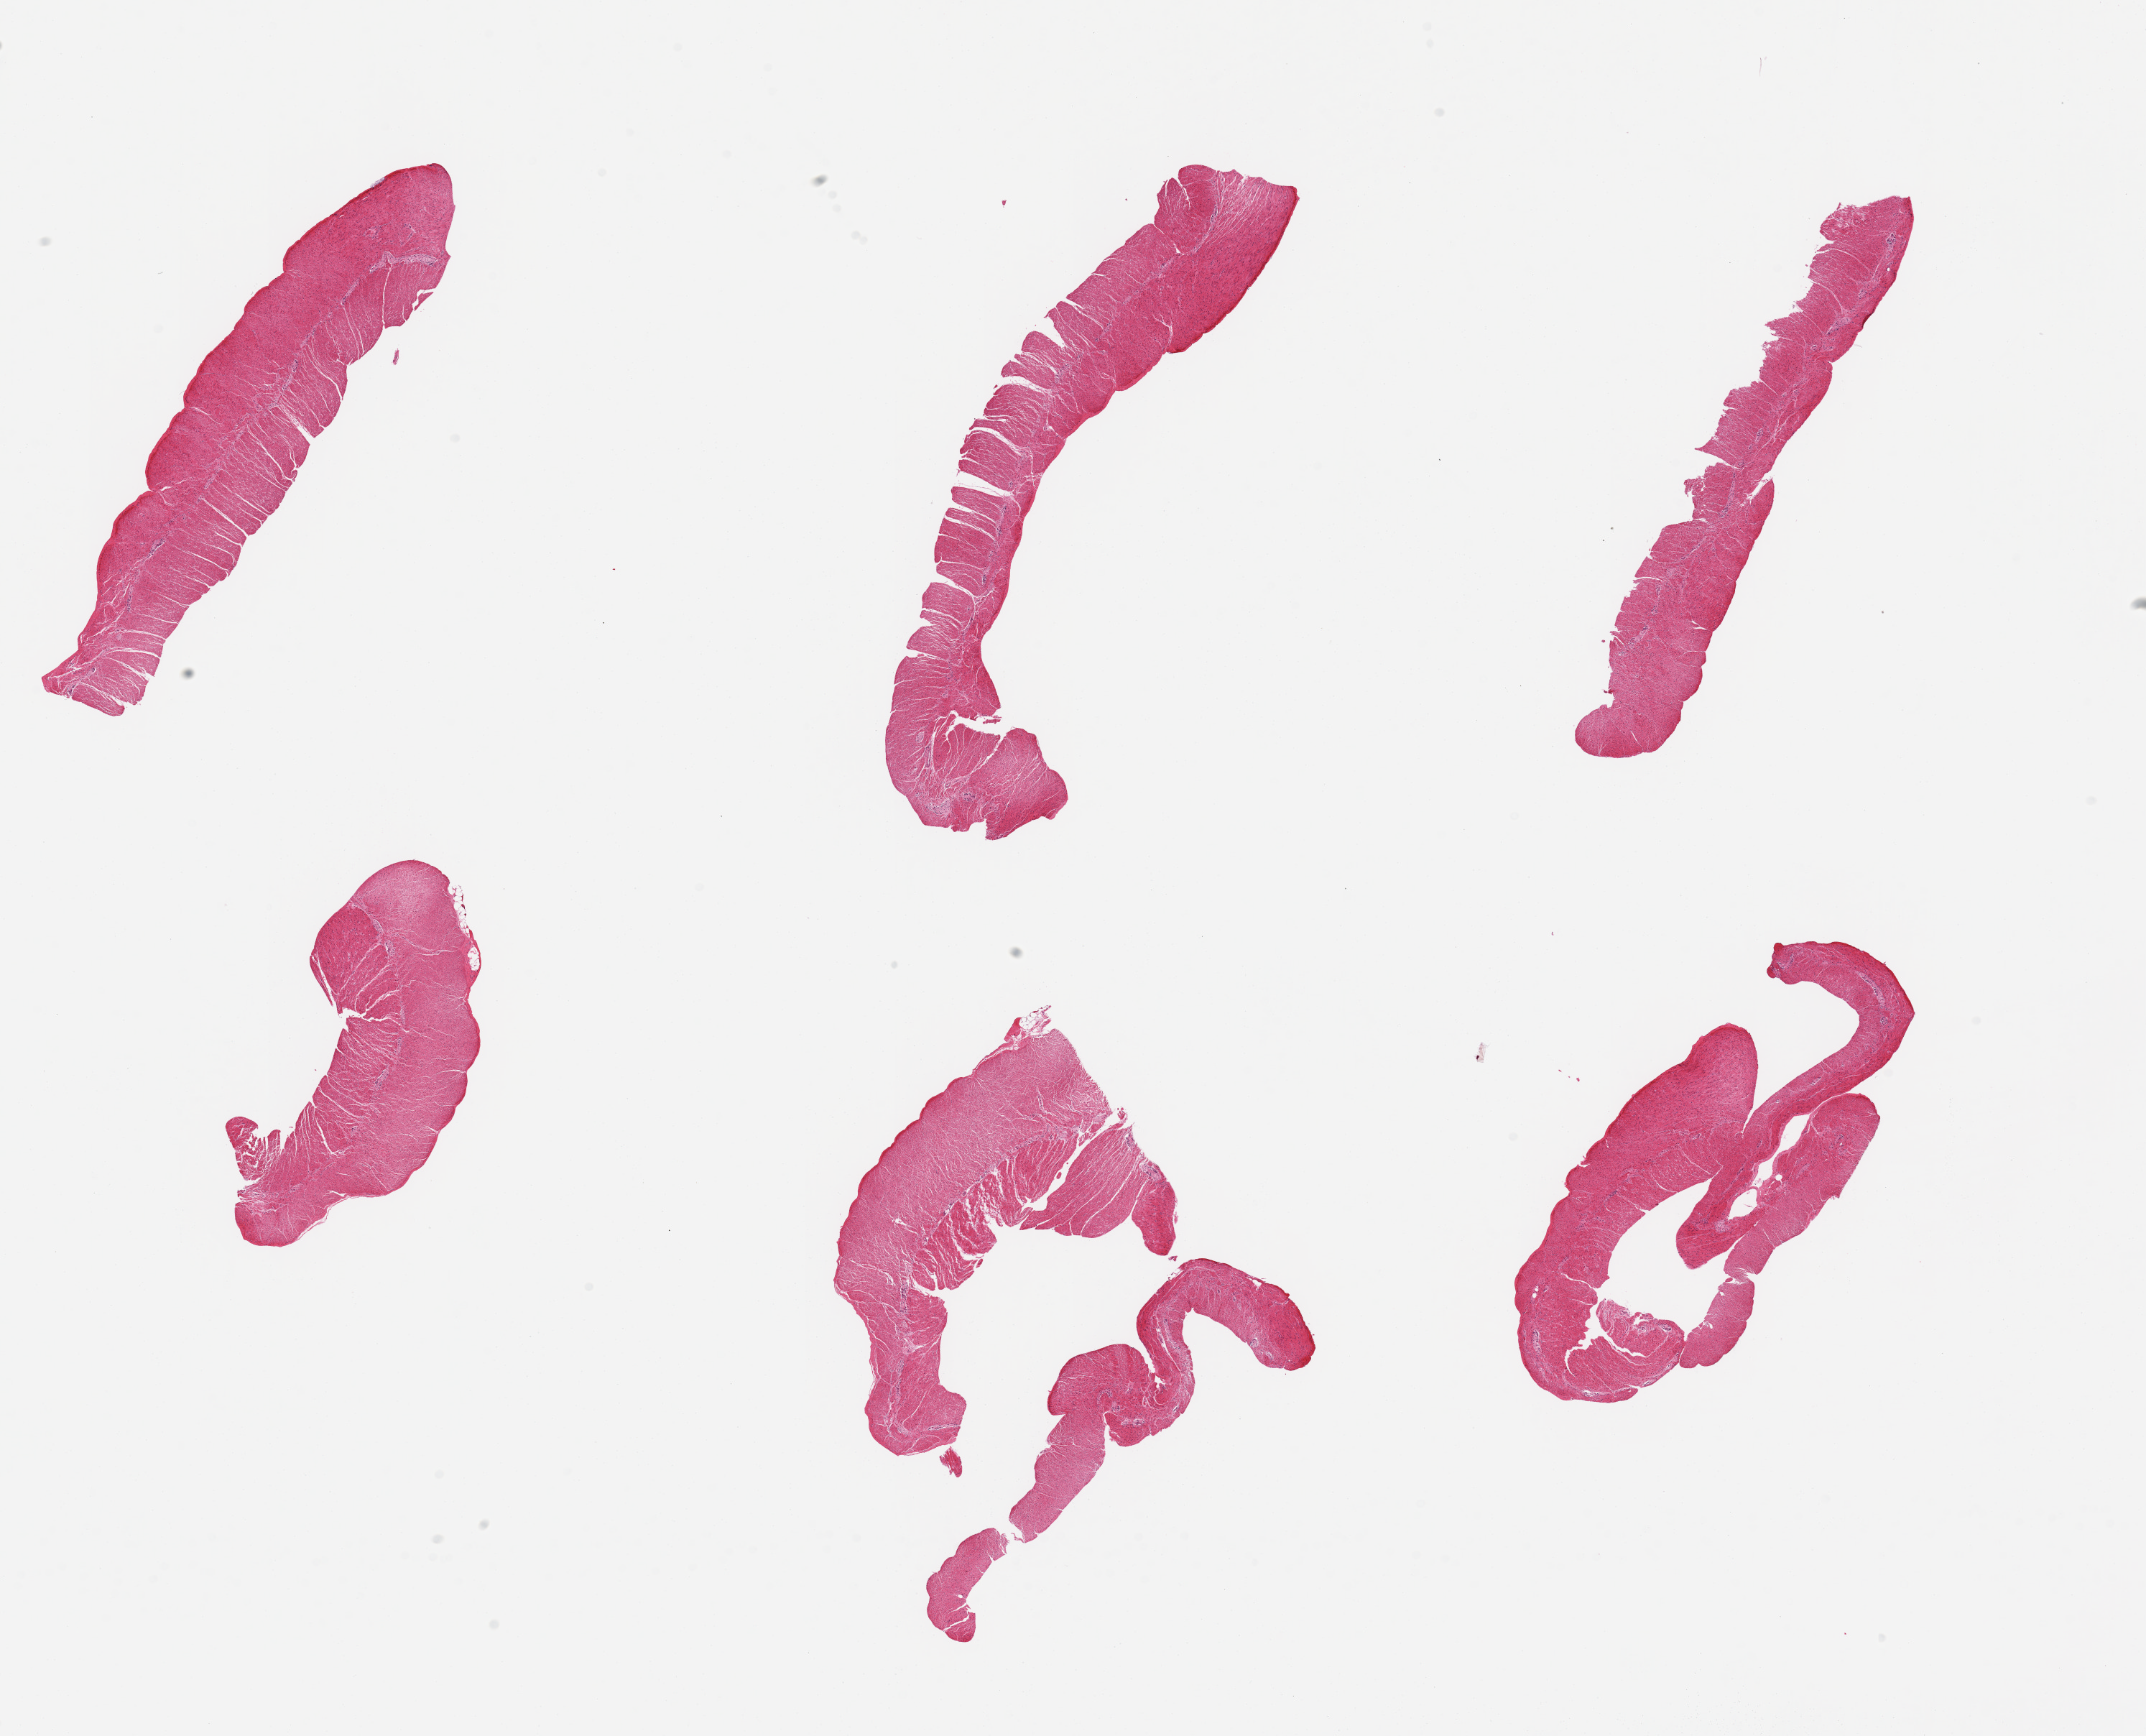
Whole-slide image, hematoxylin and eosin (H&E) stain, brightfield — whole scanned area (about 23.6 x 19.1 mm, acquisition: 20x scan) shown as a low-resolution overview; PAXgene-fixed, paraffin-embedded tissue; target tissue: sigmoid colon; tissue donor sample. Donor: male.
- pathologist's review note for this sample: 6 pieces; well dissected muscle; no fibrosis